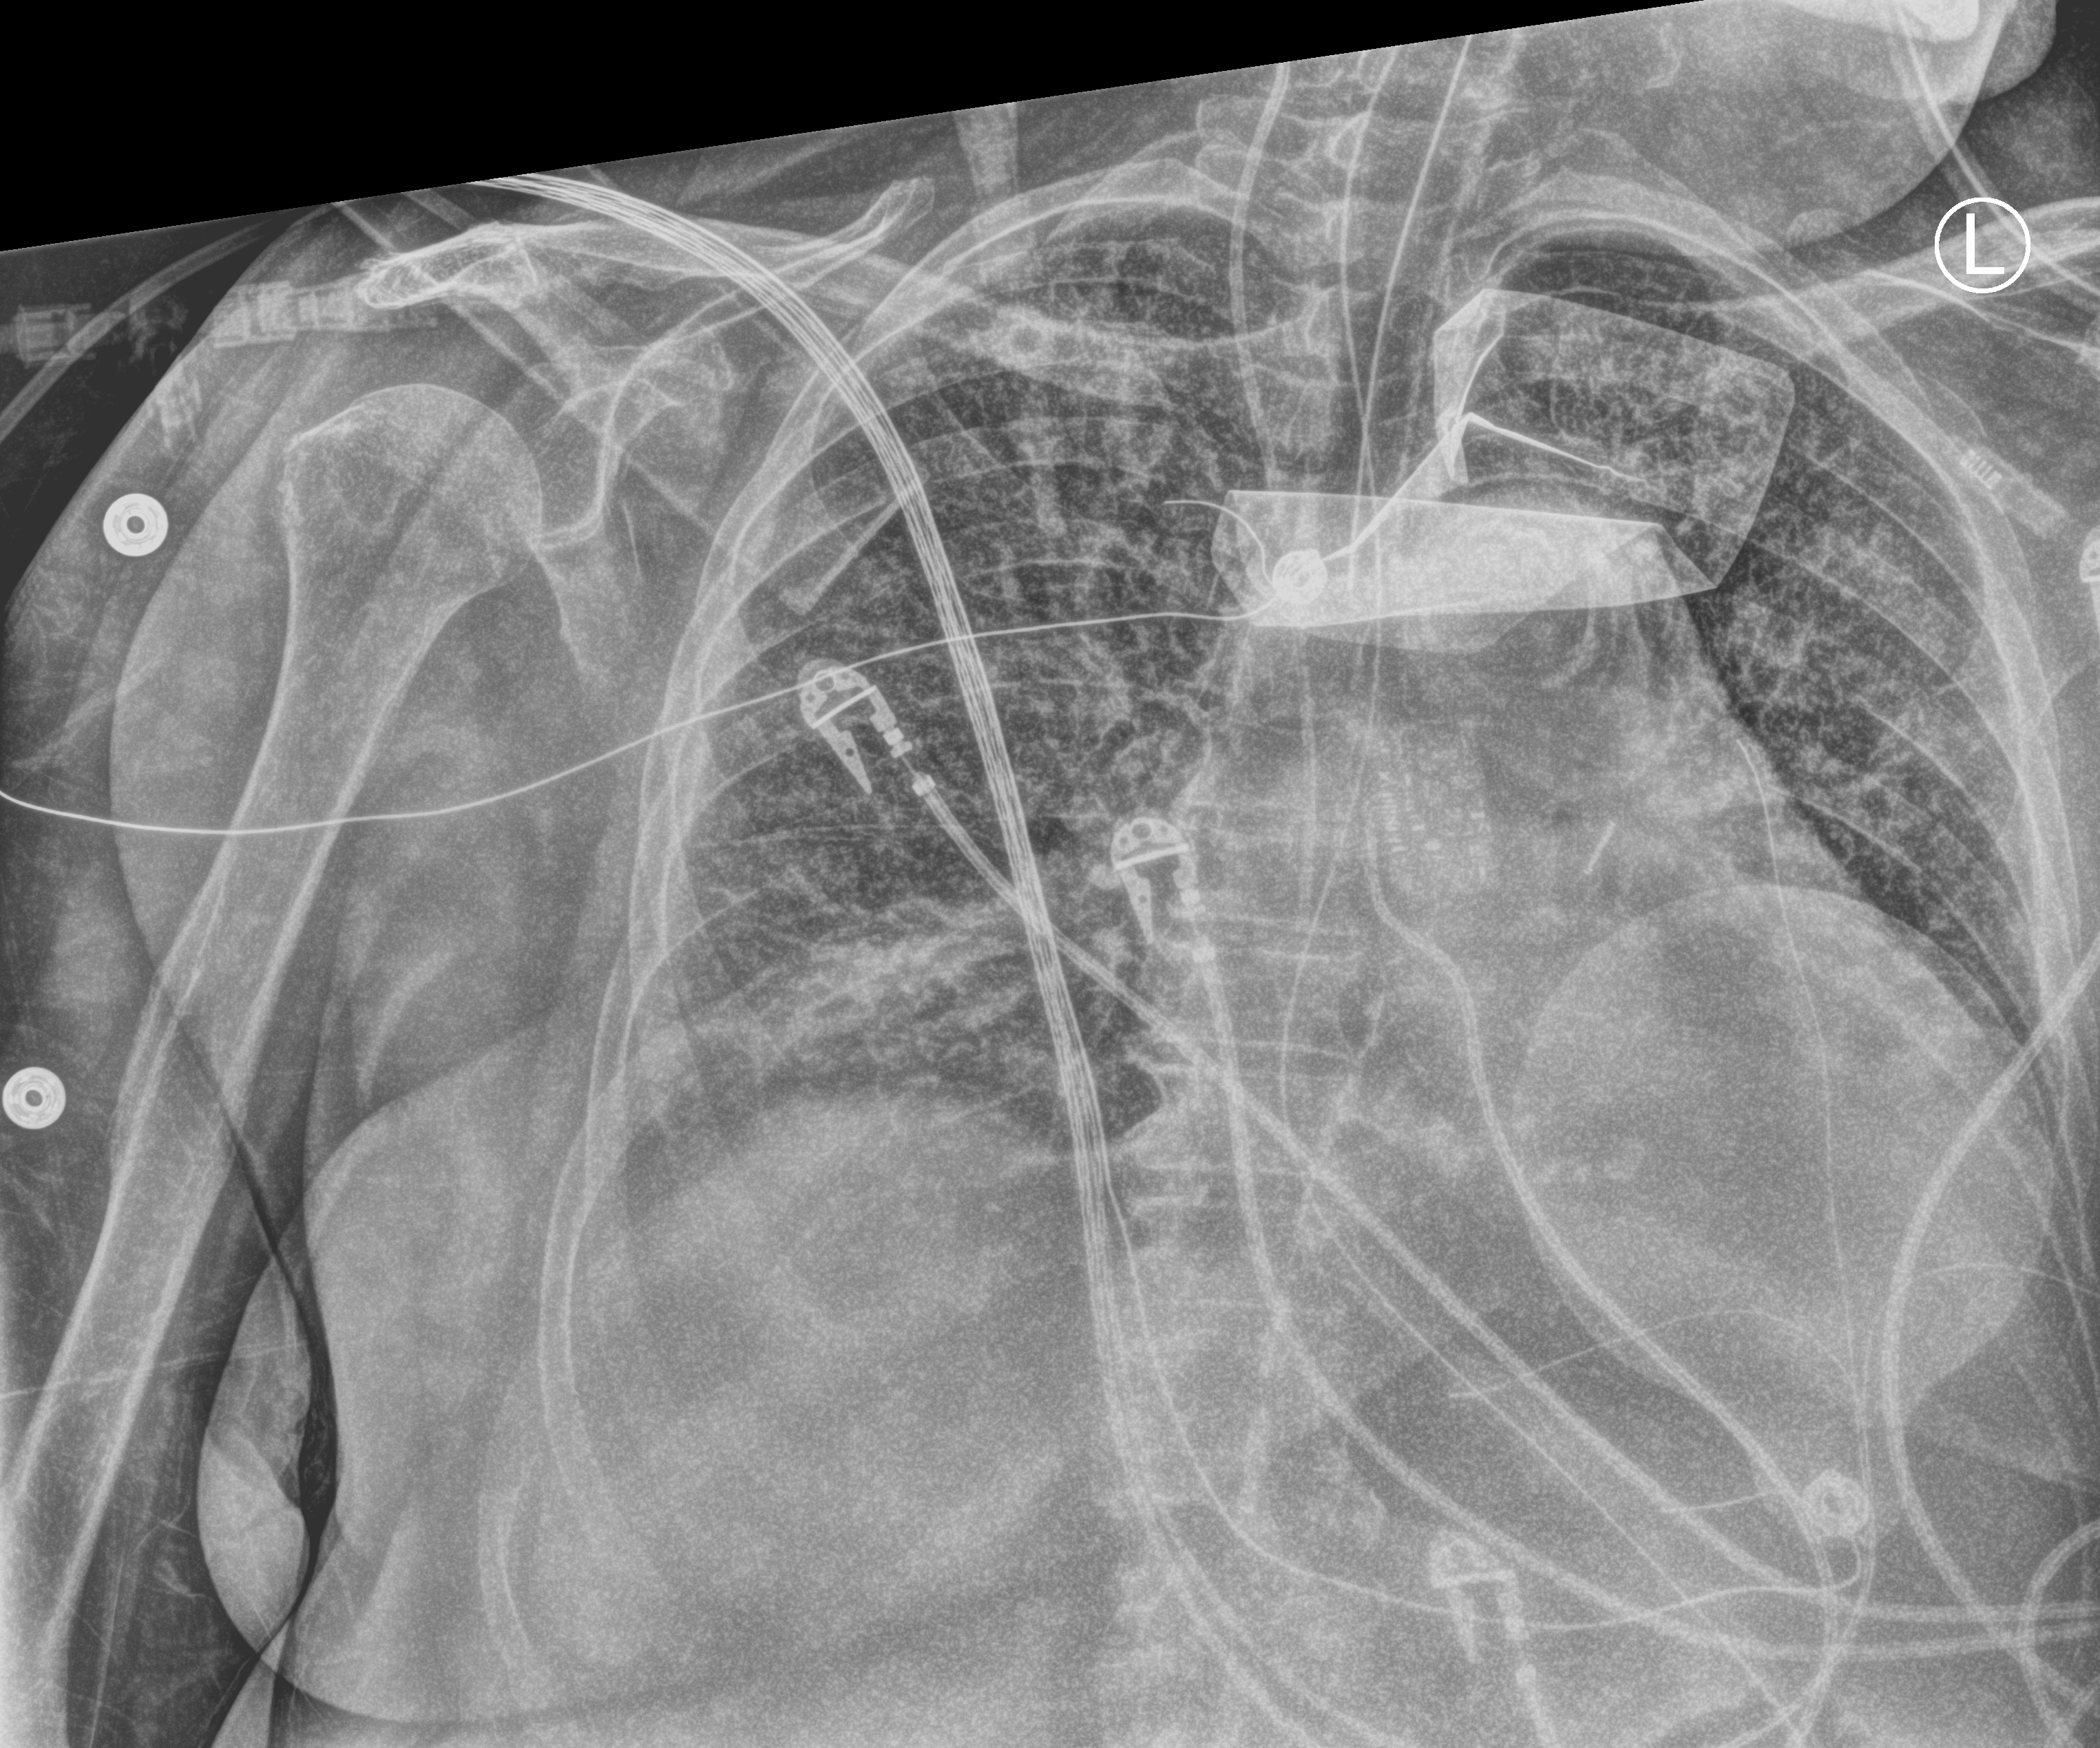
Chest X-ray (portable); anteroposterior (AP) projection. Female patient hospitalised with COVID-19, age 75–90 years.
Admission-level facts for this patient (not findings on this image; timing relative to this image not recorded):
- admitted to intensive care during this hospital stay: yes
- mechanically ventilated during this hospital stay: yes